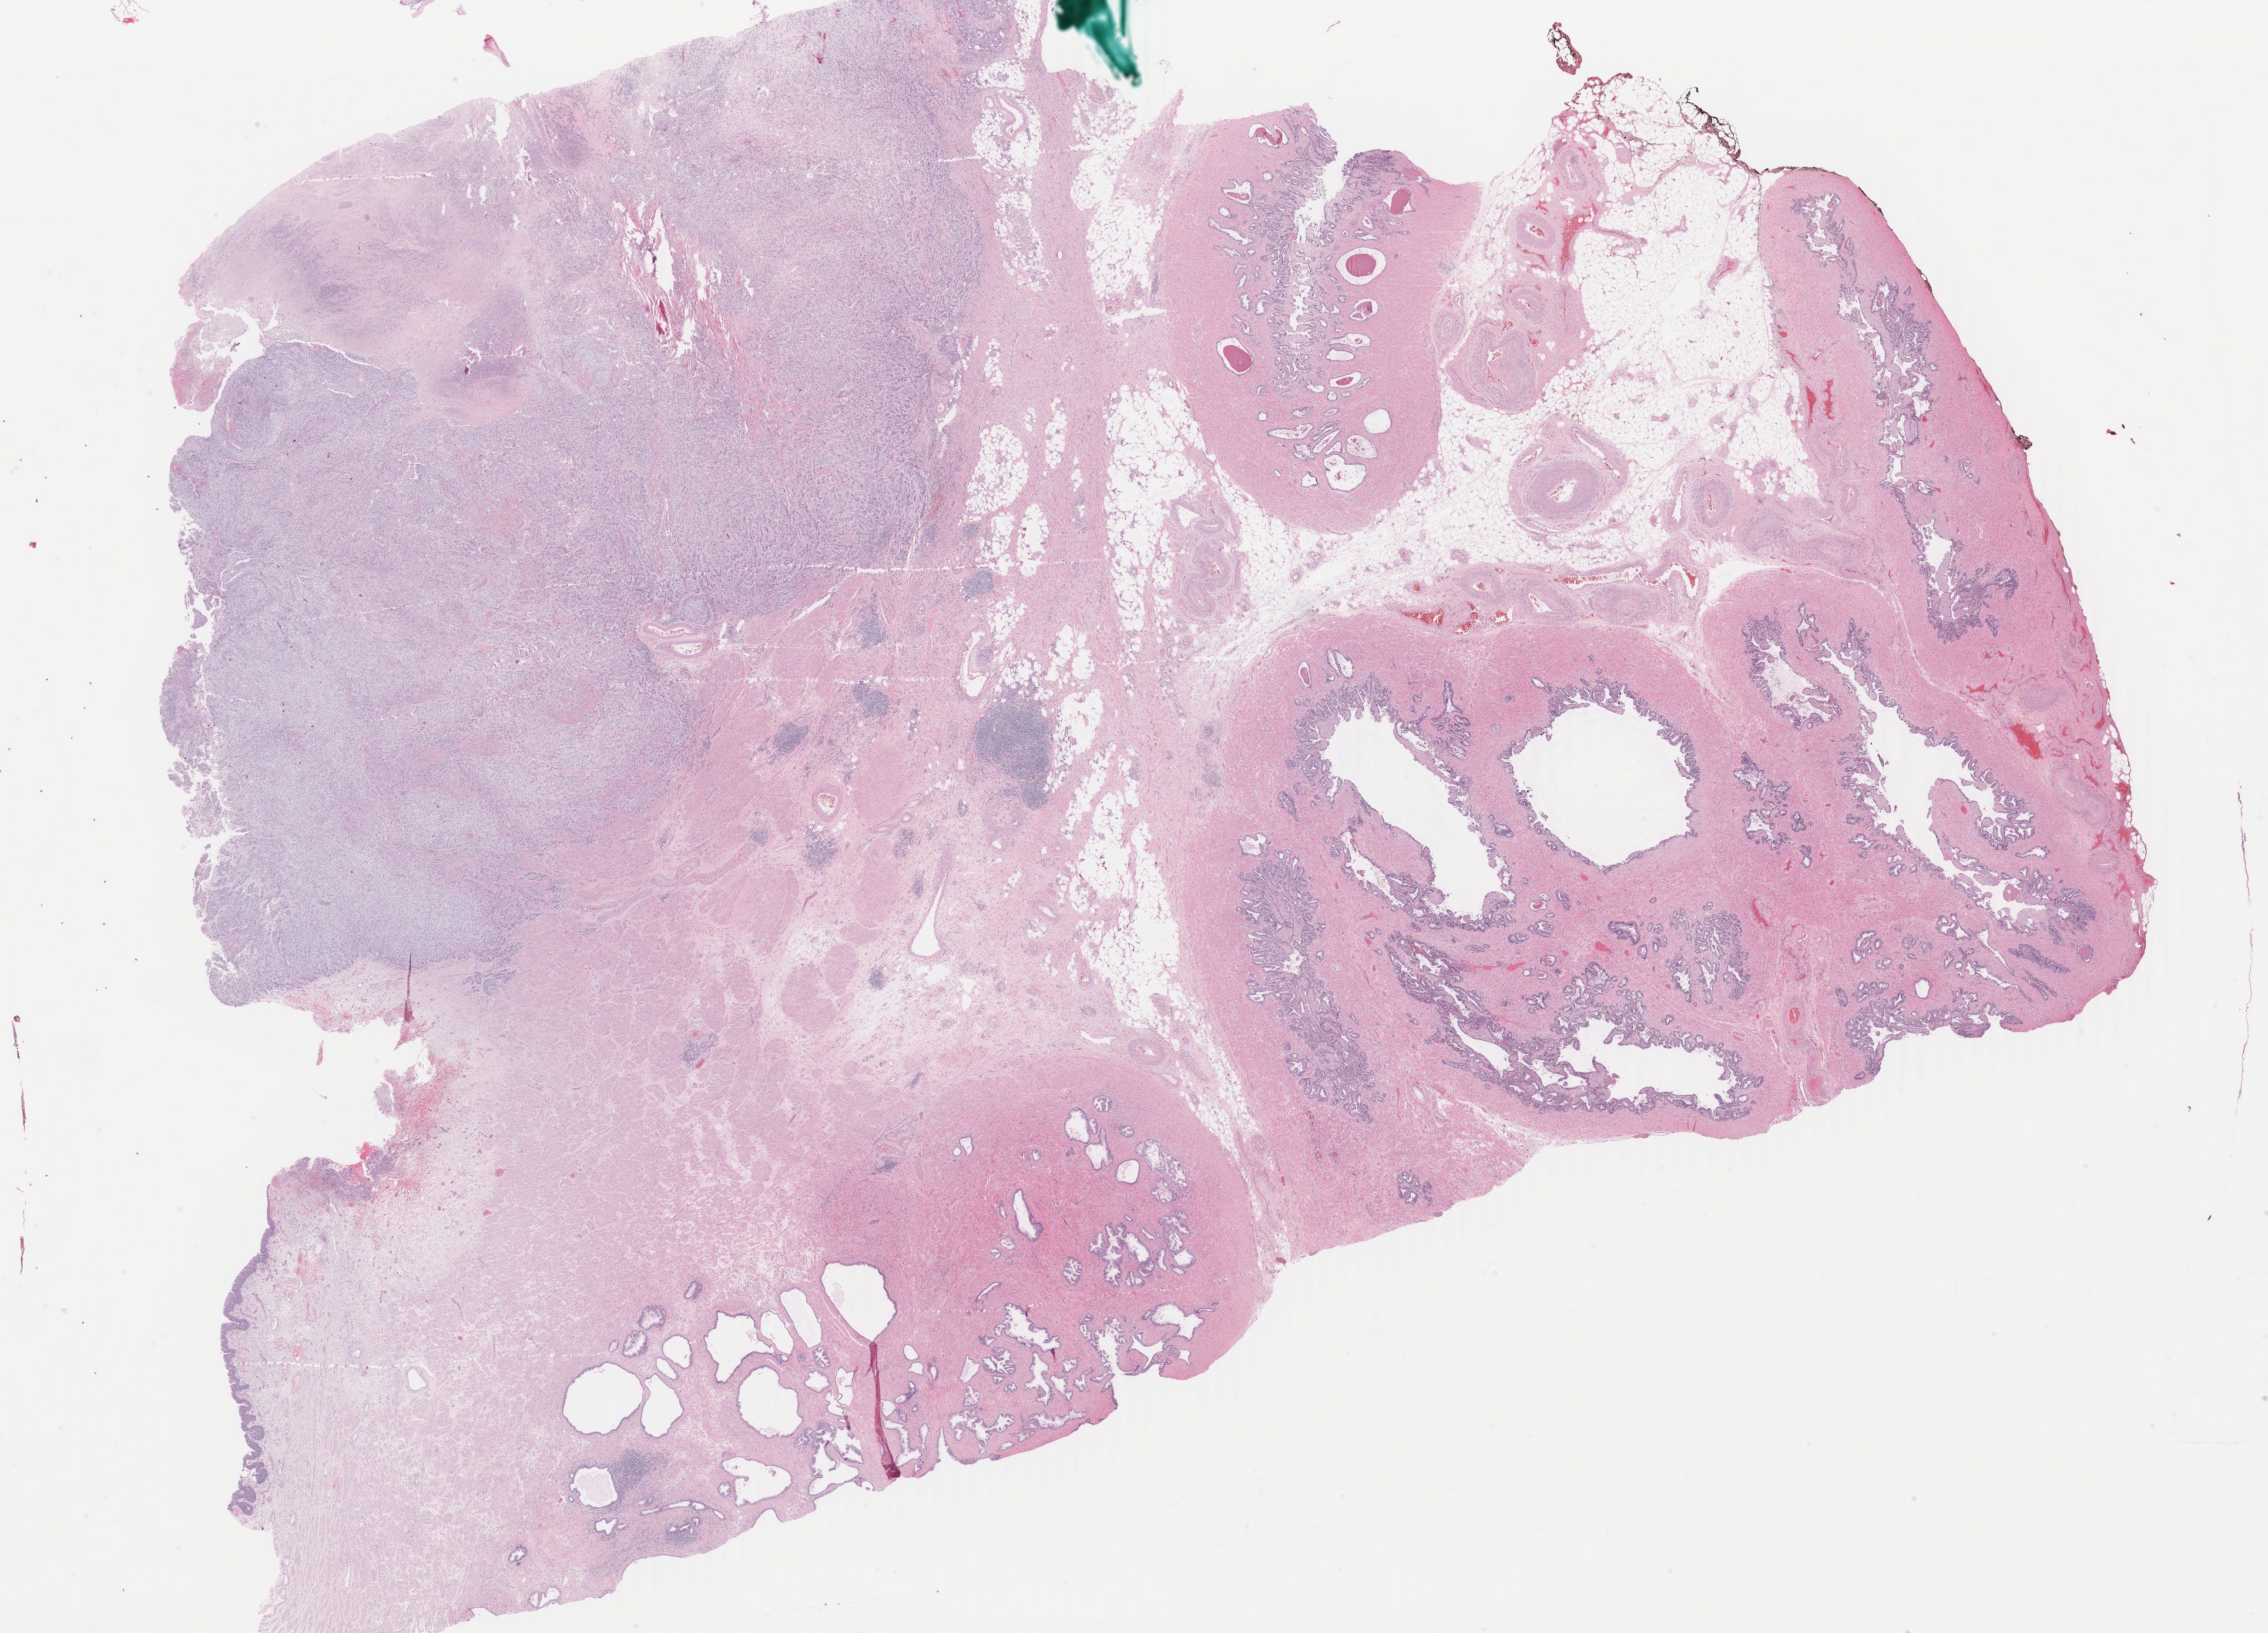
Whole-slide histology image, H&E, shown as a low-resolution overview of the whole scanned area (about 30.7 x 22.1 mm). Formalin-fixed paraffin-embedded (FFPE) diagnostic section. Primary tumour sample from the bladder. Patient: male, age at initial diagnosis 79 years.
Diagnosis: Transitional cell carcinoma (trigone of bladder).